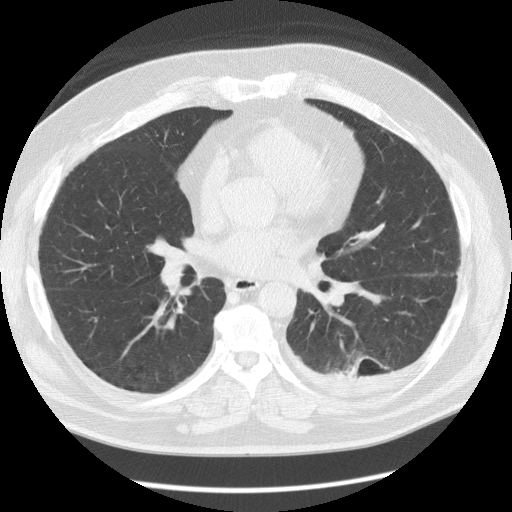
Low-dose screening chest CT, one axial slice. Reconstruction kernel STANDARD. 120 kVp. Lung window (W 1500 / L -600 HU). 2.5 mm slice thickness. 512 × 512 image matrix, field of view 370 × 370 mm.
Outlined on this slice (outlined manually by an expert reader):
- lesion 1 (tumor, lower lobe of left lung): bounding box [x1, y1, x2, y2] px = [347, 356, 369, 378]